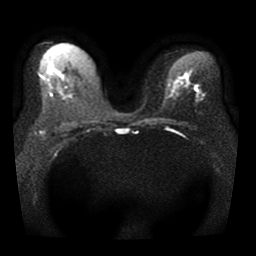
Breast MRI, one axial slice; slice 21 of 41 in the series (ordered by position); diffusion-weighted series; image 2 of 4 stored at this slice position (different b-values; order by instance number); 1.5 T; 5 mm slice thickness; 256 × 256 image matrix. Female patient.
Outlined on this slice (outlined manually by an expert reader):
- tumour on diffusion-weighted imaging: box from (x=195, y=86) to (x=199, y=92) px